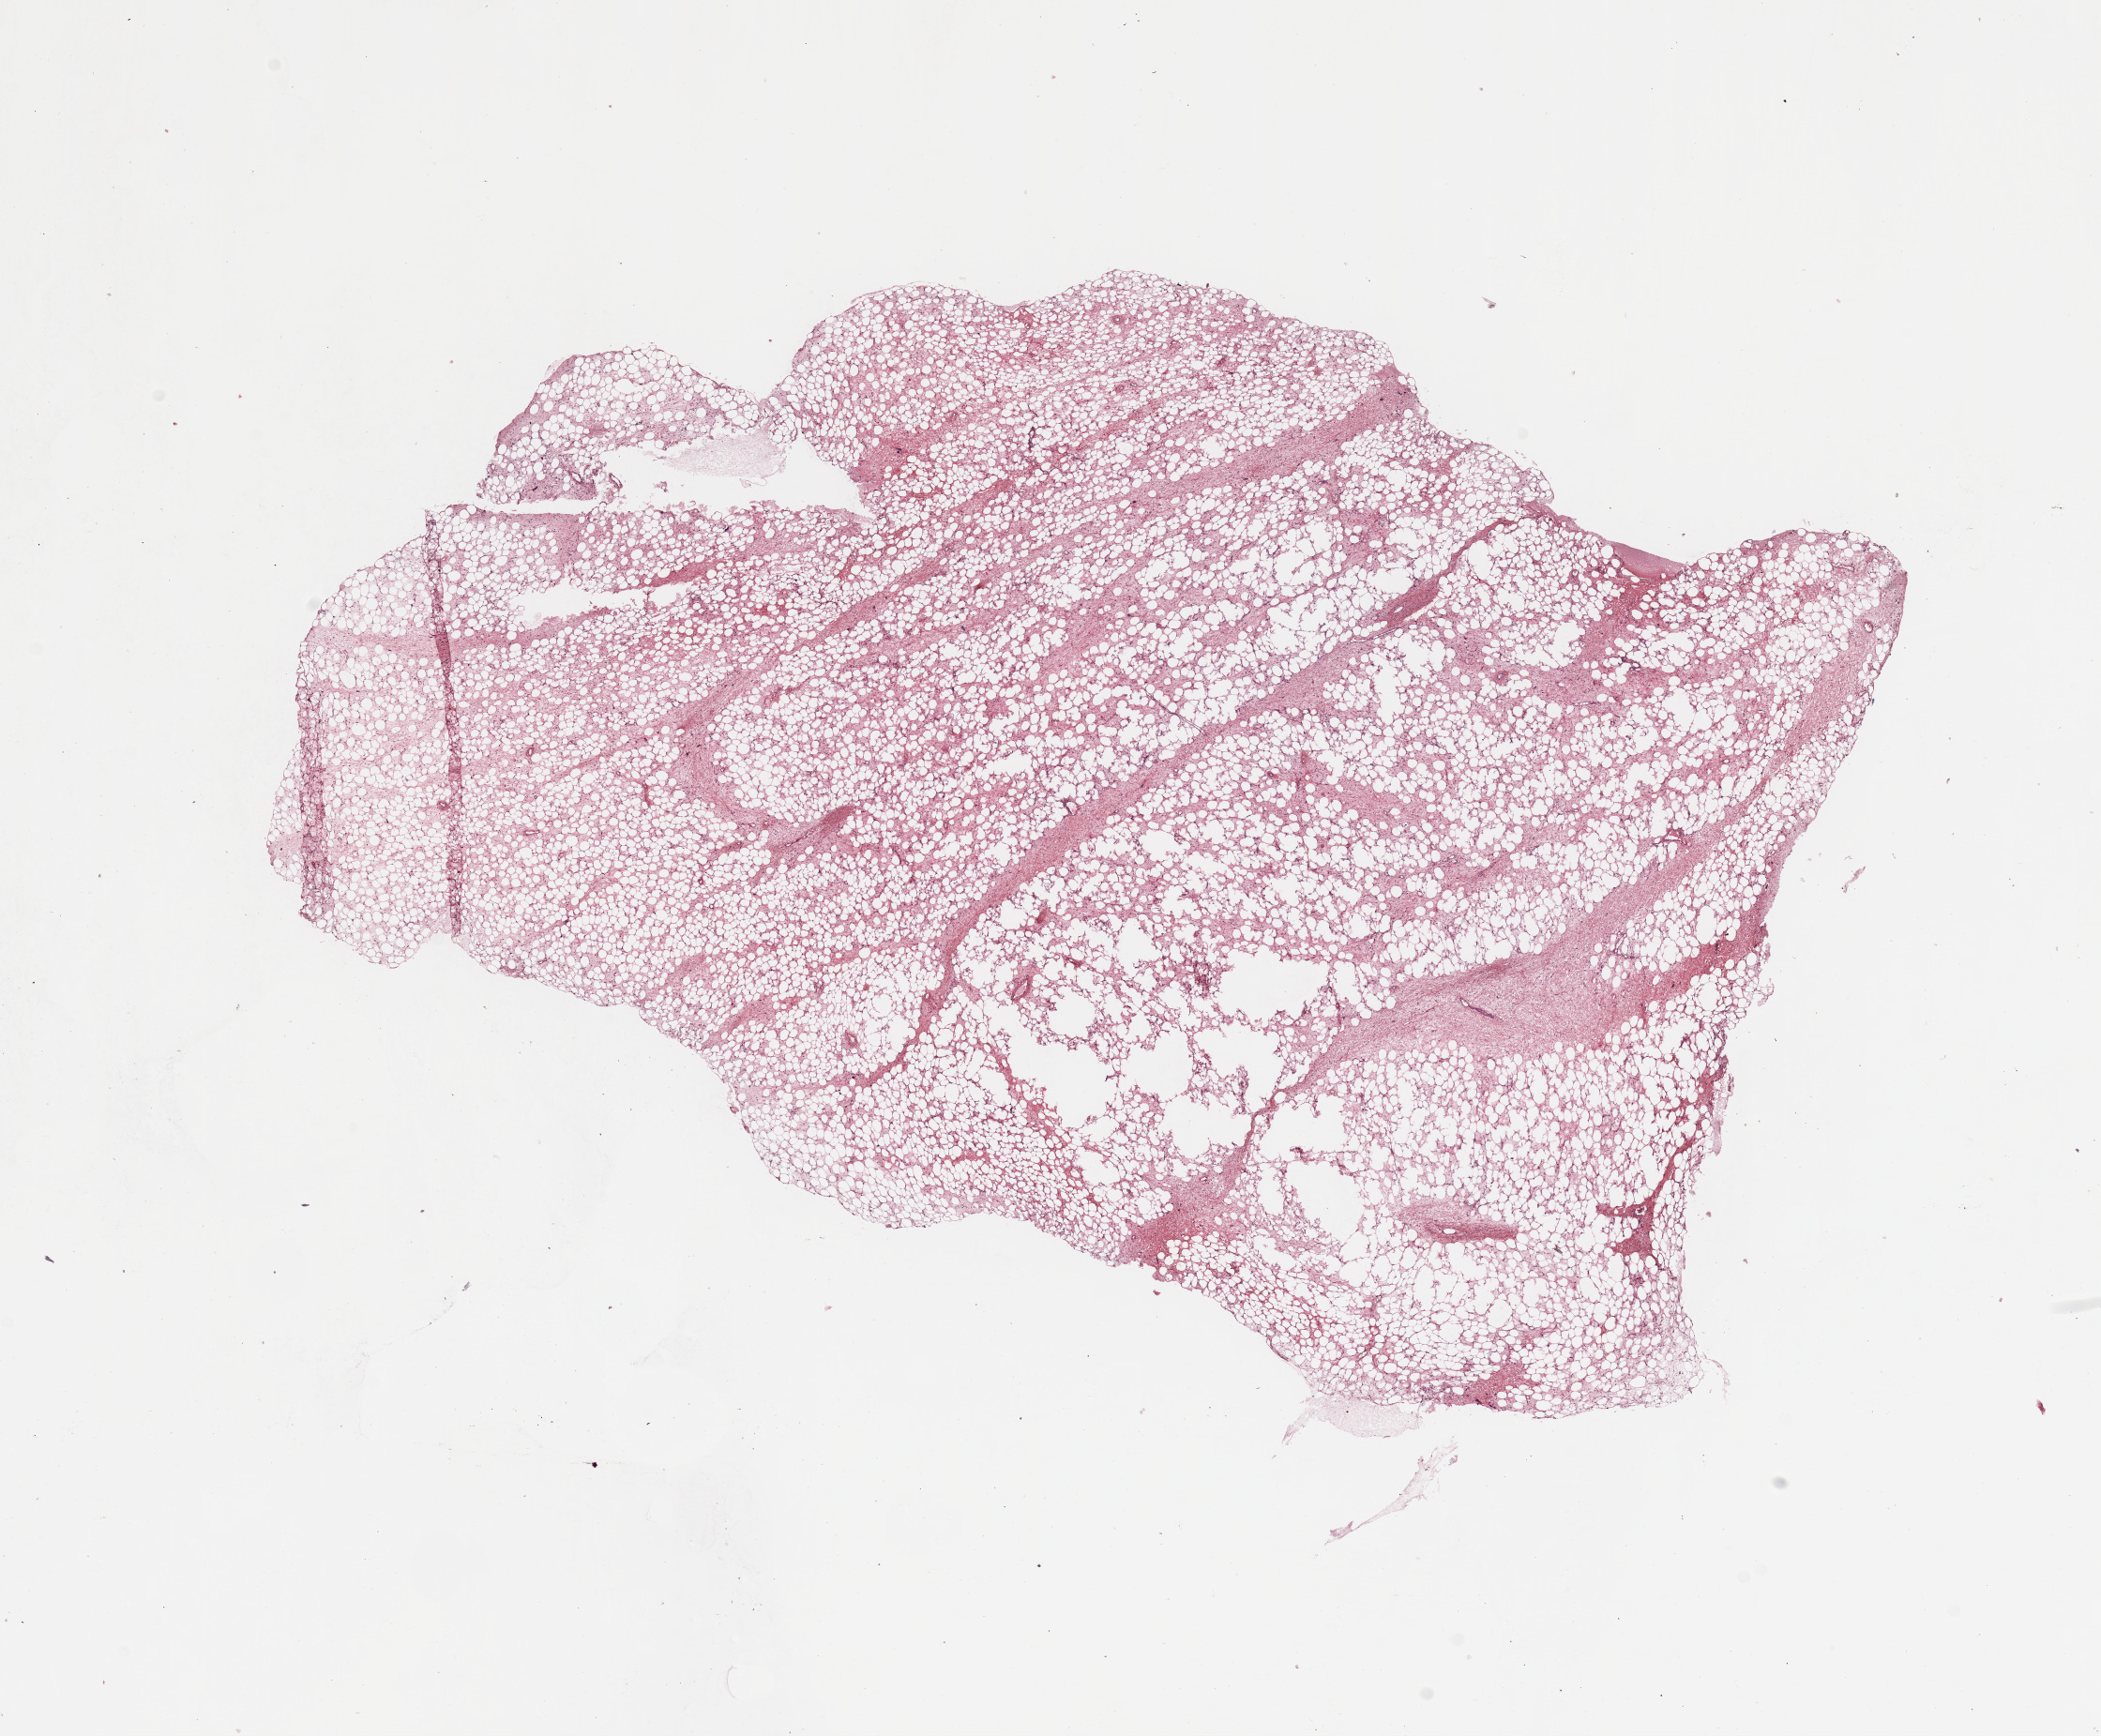
Whole-slide histology image, H&E-stained, a low-resolution overview of the entire scanned area, about 17.7 x 14.6 mm; tumour tissue sample. 65-year-old female patient.
Patient diagnosis (cohort enrolment): sarcoma (site not recorded at cohort level).